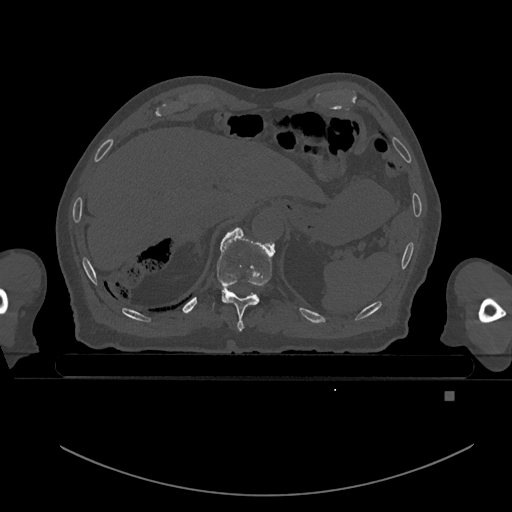
CT including the spine, one axial slice; position 81 of 969 along the scan axis; bone window (W 1800 / L 400 HU); 0.5 mm slice thickness; 512 × 512 image matrix, field of view 456 × 456 mm. Male patient, age 82 years. From the clinical record (not read from this slice): primary cancer: prostate.
Structures marked on this image (semi-automatically segmented with operator editing):
- T10 vertebra: bounding box <211,228,275,331> (left, top, right, bottom; pixels)